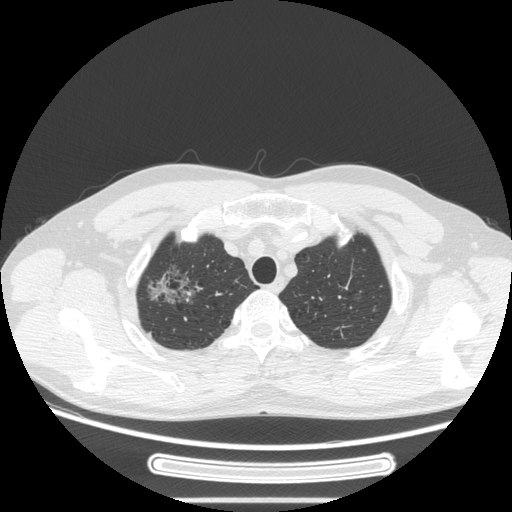
Chest CT, one axial slice; position 226 of 269 along the scan axis; 120 kVp; lung window (W 1500 / L -600 HU); 512 × 512 image matrix, field of view 382 × 382 mm. Patient: male, 53 years. From the clinical record (not read from this slice): clinical TNM (as recorded): T1c N0 M0; histopathological grade: G2.
Structures marked on this image (rectangle marked by the reading radiologist):
- lung tumour (recorded histology: adenocarcinoma): bounding box [x1, y1, x2, y2] px = [138, 255, 201, 308]